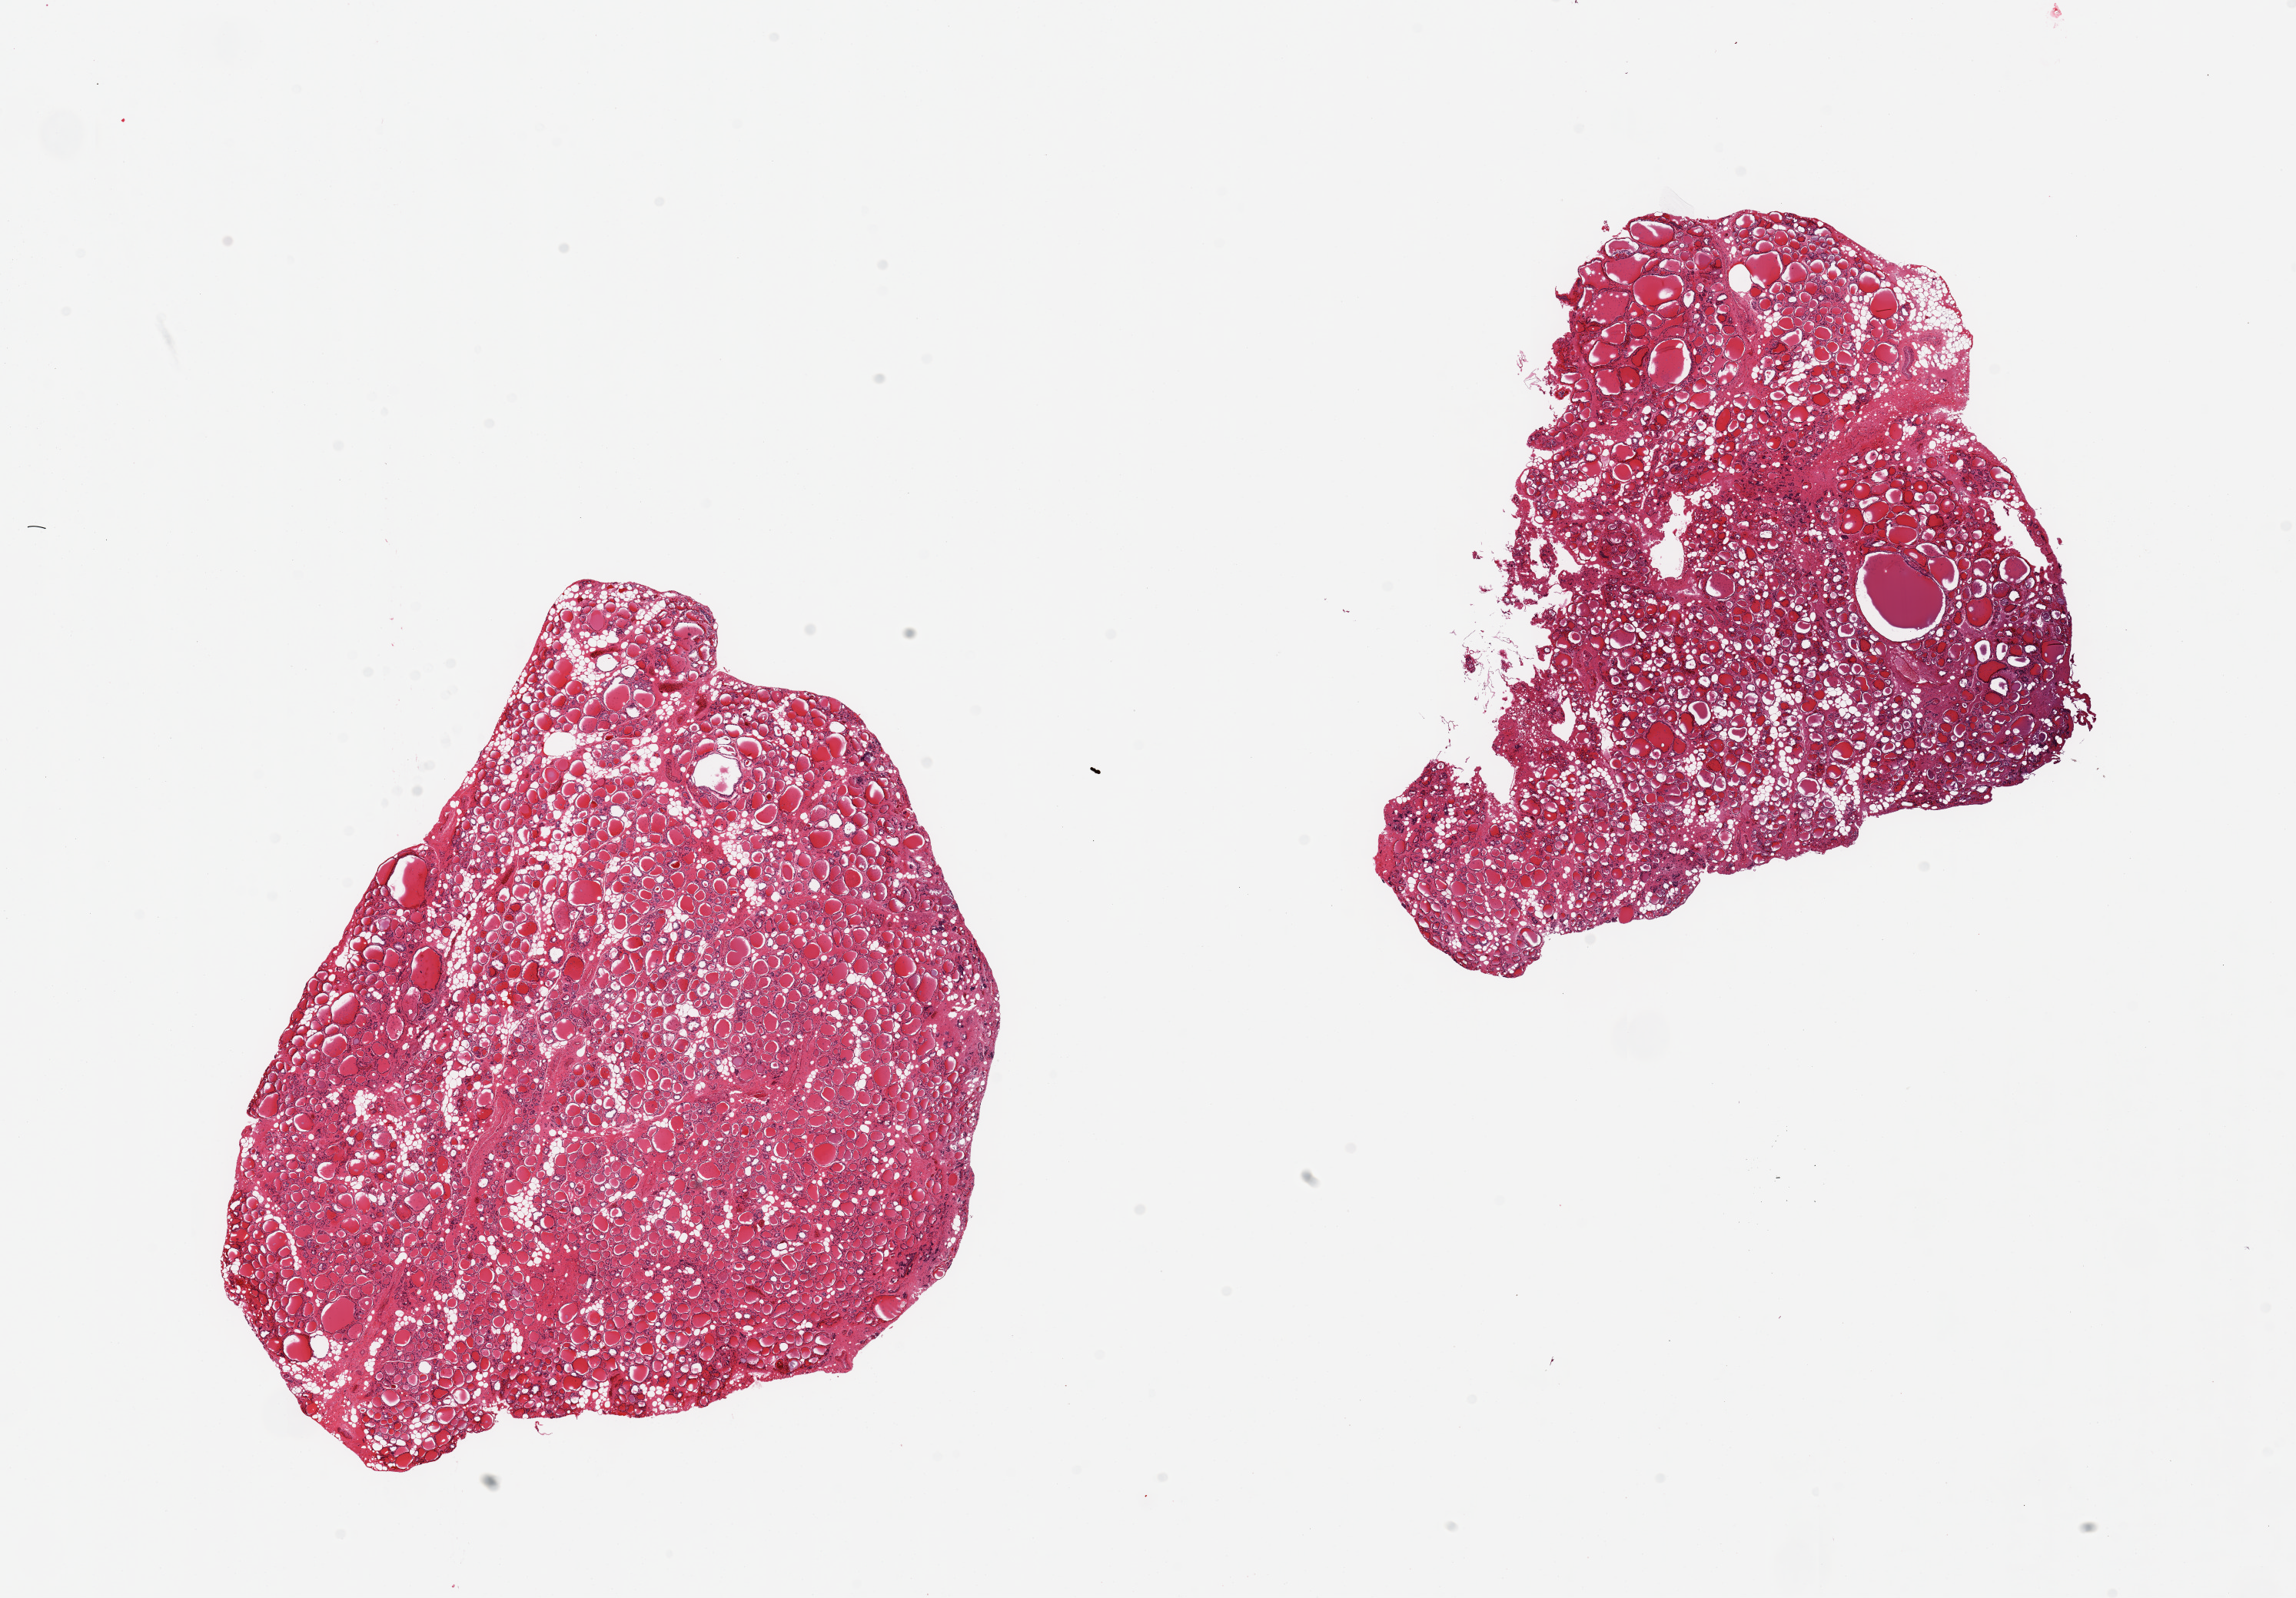
Digitized hematoxylin and eosin (H&E)-stained section, shown as a low-resolution overview of the whole scanned area (about 23.6 x 16.4 mm), PAXgene-fixed, paraffin-embedded tissue, section of thyroid (target tissue), donor tissue sample.
Reviewer comment on this tissue sample: 2 pieces; 20% diffusely distributed internal fat.